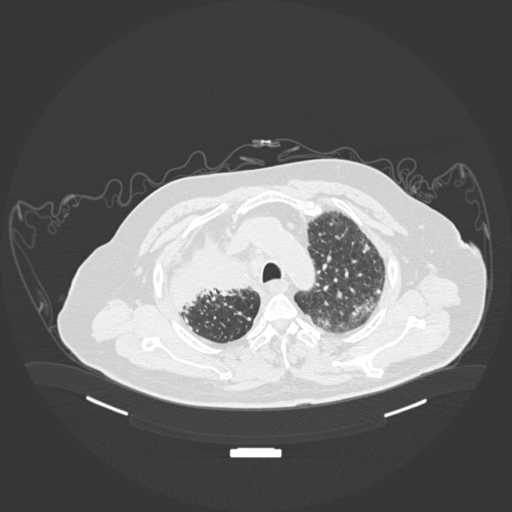
Chest CT, one axial slice; slice 147 of 201 in the series (ordered by position); lung window (W 1500 / L -600 HU); 1 mm slice thickness; 512 × 512 image matrix. Patient: male, 69 years. Case-level facts recorded for this patient, not image findings: clinical TNM (as recorded): T4 N3 M1.
Structures marked on this image (bounding box drawn by a radiologist):
- lung tumour (recorded histology: adenocarcinoma): bounding box [x1, y1, x2, y2] px = [162, 228, 253, 315]